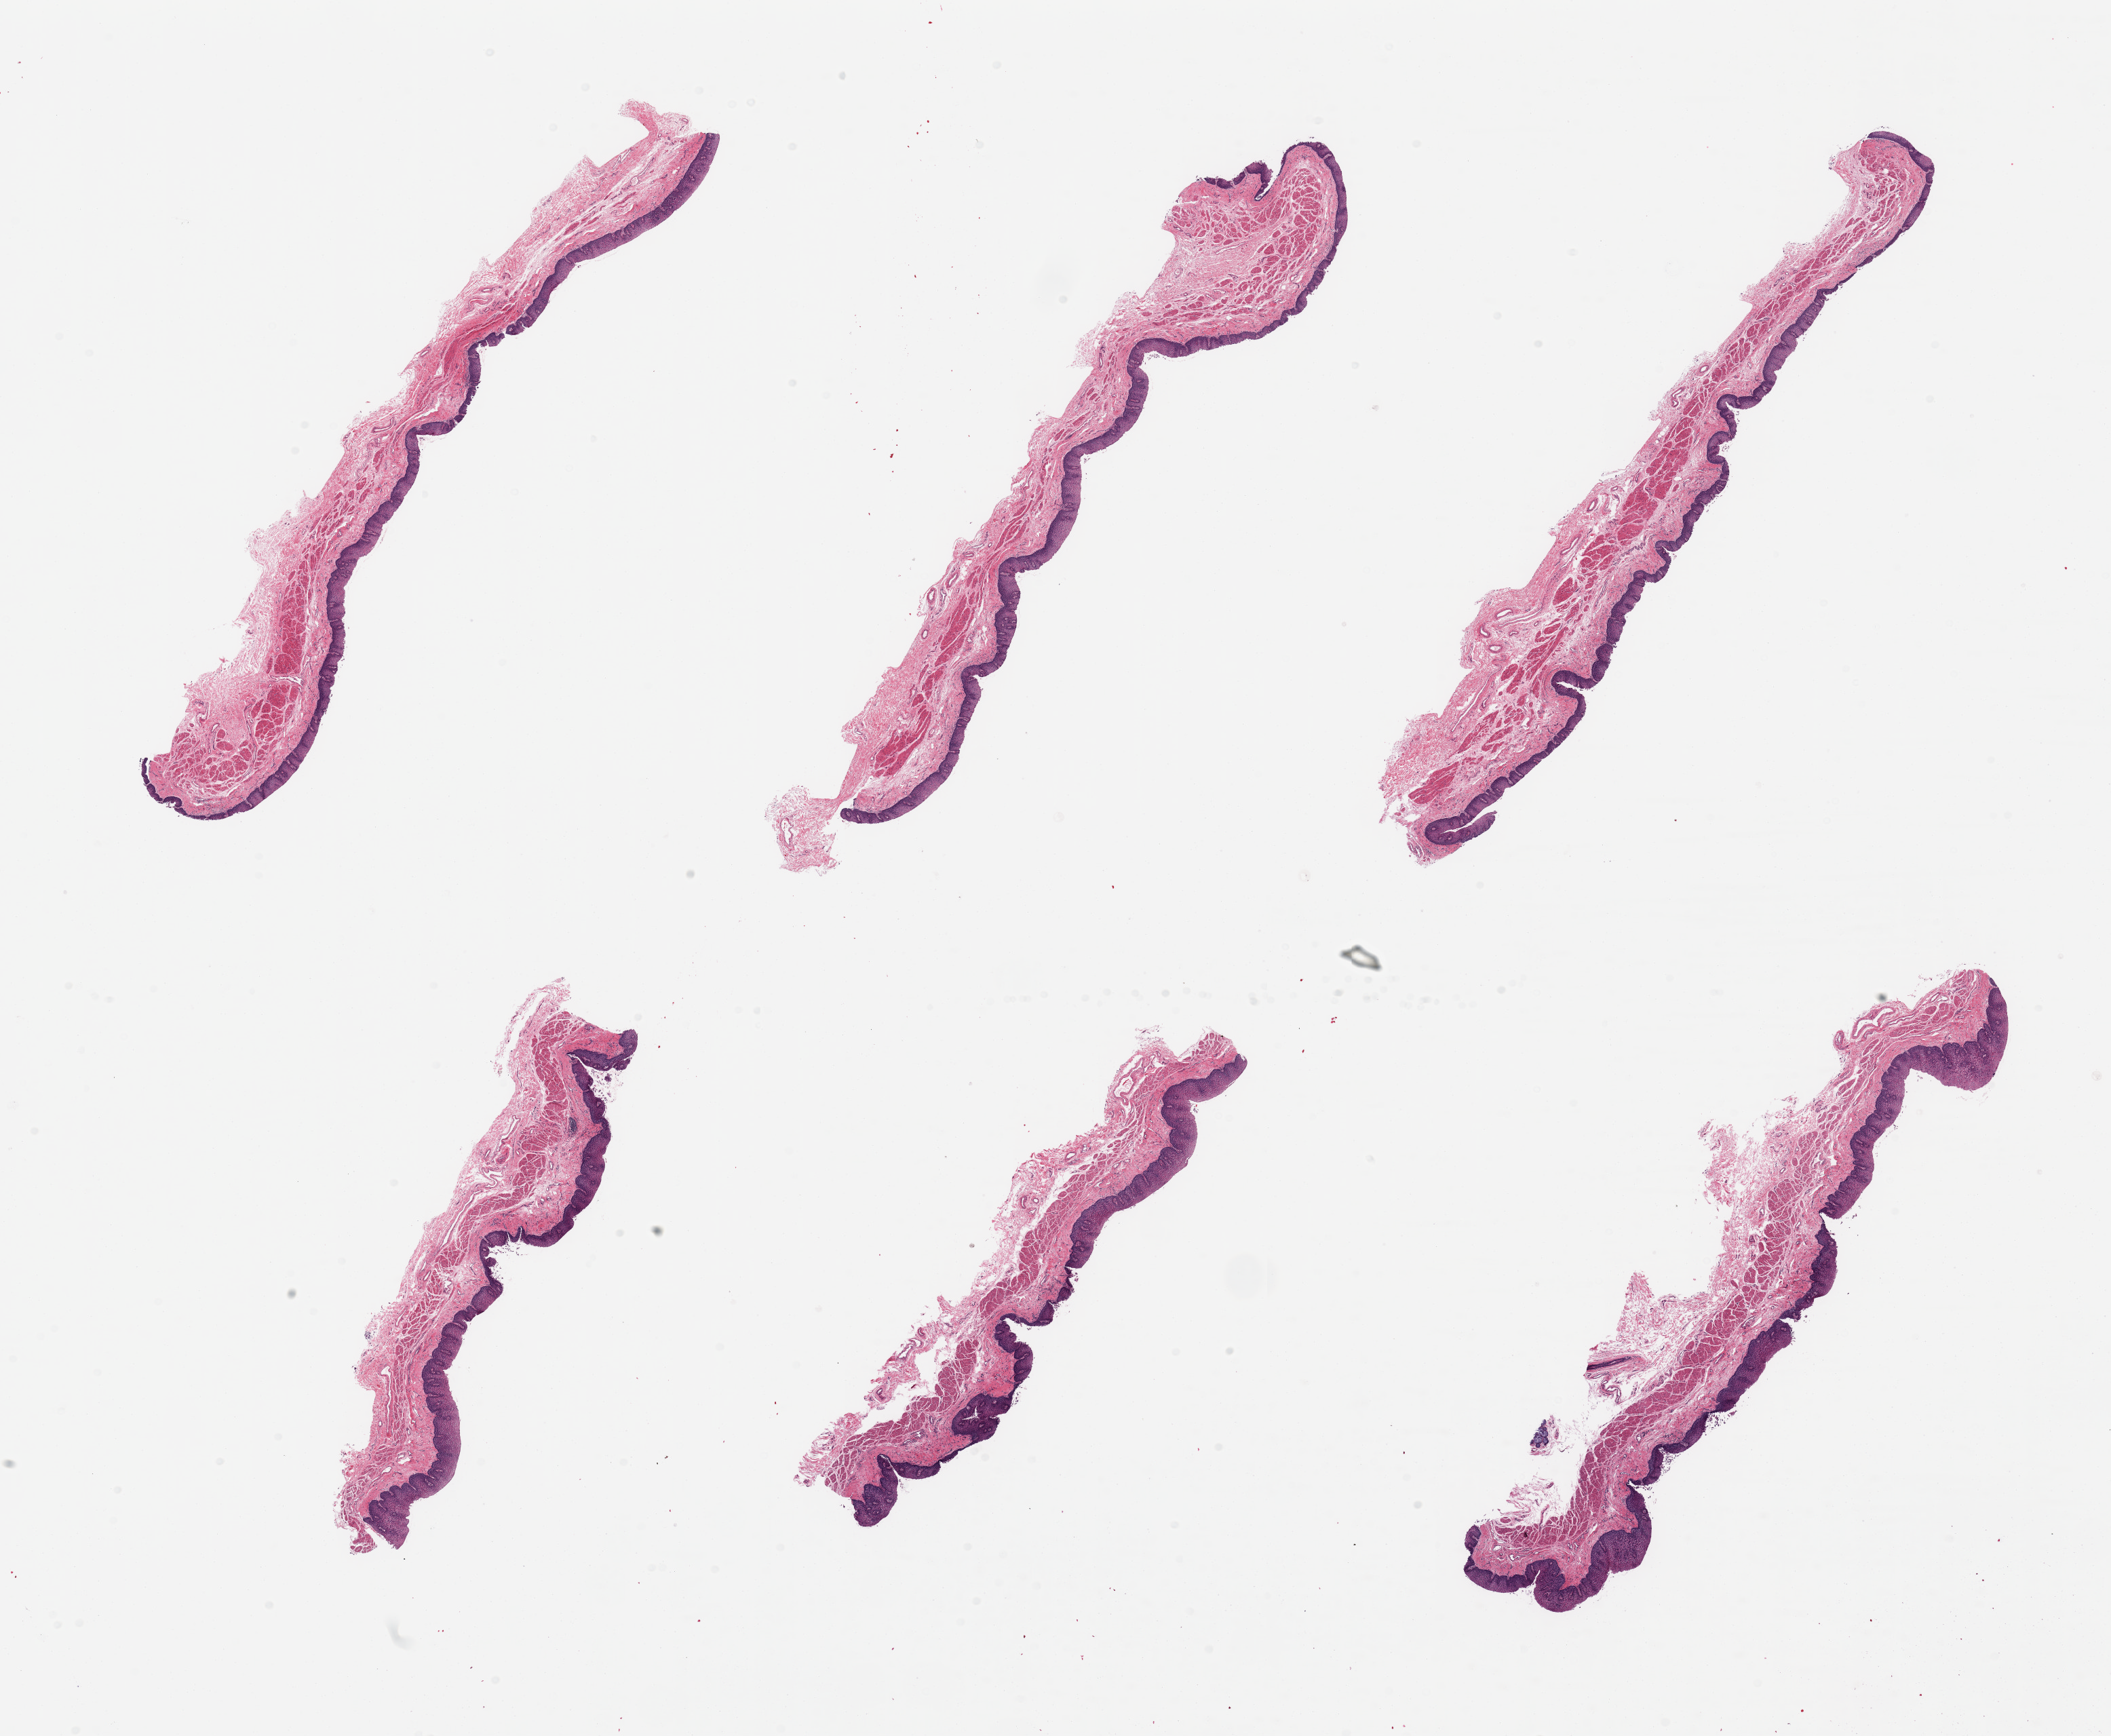
Digitized haematoxylin and eosin-stained section, brightfield — shown as a low-resolution overview of the whole scanned area (about 24.6 x 20.2 mm), PAXgene-fixed, paraffin-embedded tissue, section of esophageal mucous membrane (target tissue), tissue donor sample. Donor sex: female.
Review note (as recorded): 6 pieces, squamous mucosa is ~0.17mm, 10-15% thickness.